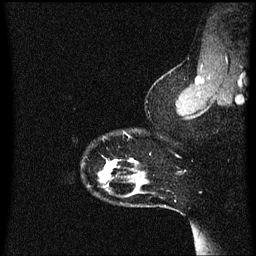
Breast MRI (dynamic contrast-enhanced), one sagittal slice; slice 53 of 60 in the series (ordered by position); dynamic contrast-enhanced series, image 2 of 3 at this slice position (ordered by acquisition); 1.5 T; TE 4.2 ms, TR 8.4 ms; 256 × 256 image matrix, field of view 200 × 200 mm. Female patient, age 33 years.
Structures marked on this image (semi-automatic segmentation, software-assisted and operator-edited):
- analysis volume of interest (the breast-tissue region the enhancement analysis was run in; not a lesion): box from (x=82, y=158) to (x=150, y=191) px
- tumour enhancement mask (voxels above the 70 % enhancement threshold inside the analysis volume of interest): (x=100, y=160)–(x=138, y=179)